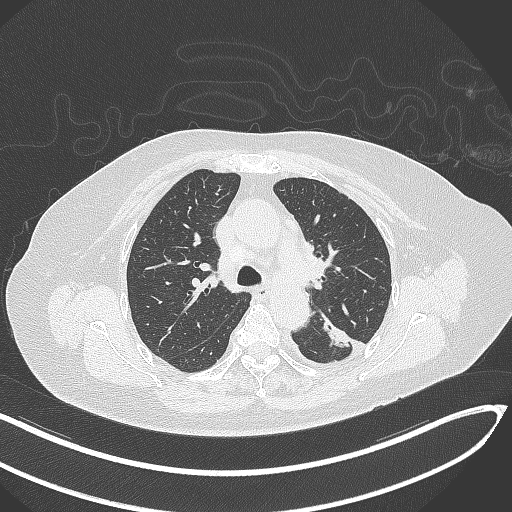
Chest CT, one axial slice. Reconstruction kernel B70f. 120 kVp. Lung window (W 1500 / L -600 HU). 1 mm slice thickness. 512 × 512 image matrix. Patient: female, 76 years. From the clinical record (not read from this slice): clinical TNM (as recorded): T1c N0 M0.
Structures marked on this image (bounding box drawn by a radiologist):
- lung tumour (recorded histology: adenocarcinoma): bounding box (x1, y1, x2, y2) in pixels: (318, 313, 356, 359)